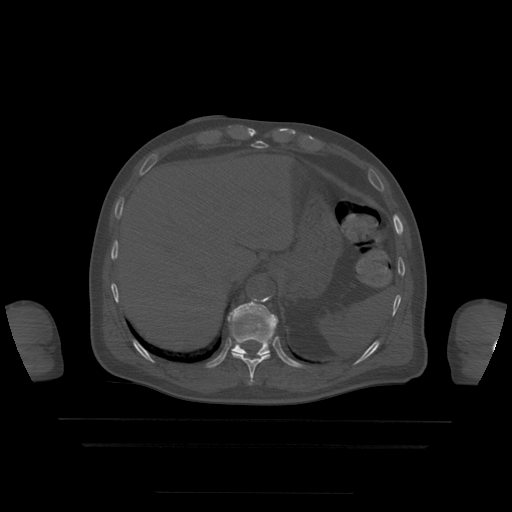
CT including the spine, one axial slice. Slice 231 of 522 in the series (ordered by position). Bone window (W 1800 / L 400 HU). 512 × 512 image matrix. Patient age 68 years. Case-level facts recorded for this patient, not image findings: primary cancer: urothelial.
Structures marked on this image (semi-automatically segmented with operator editing):
- T10 vertebra: bounding box [x1, y1, x2, y2] px = [232, 351, 270, 385]
- T11 vertebra: [228, 302, 279, 356]